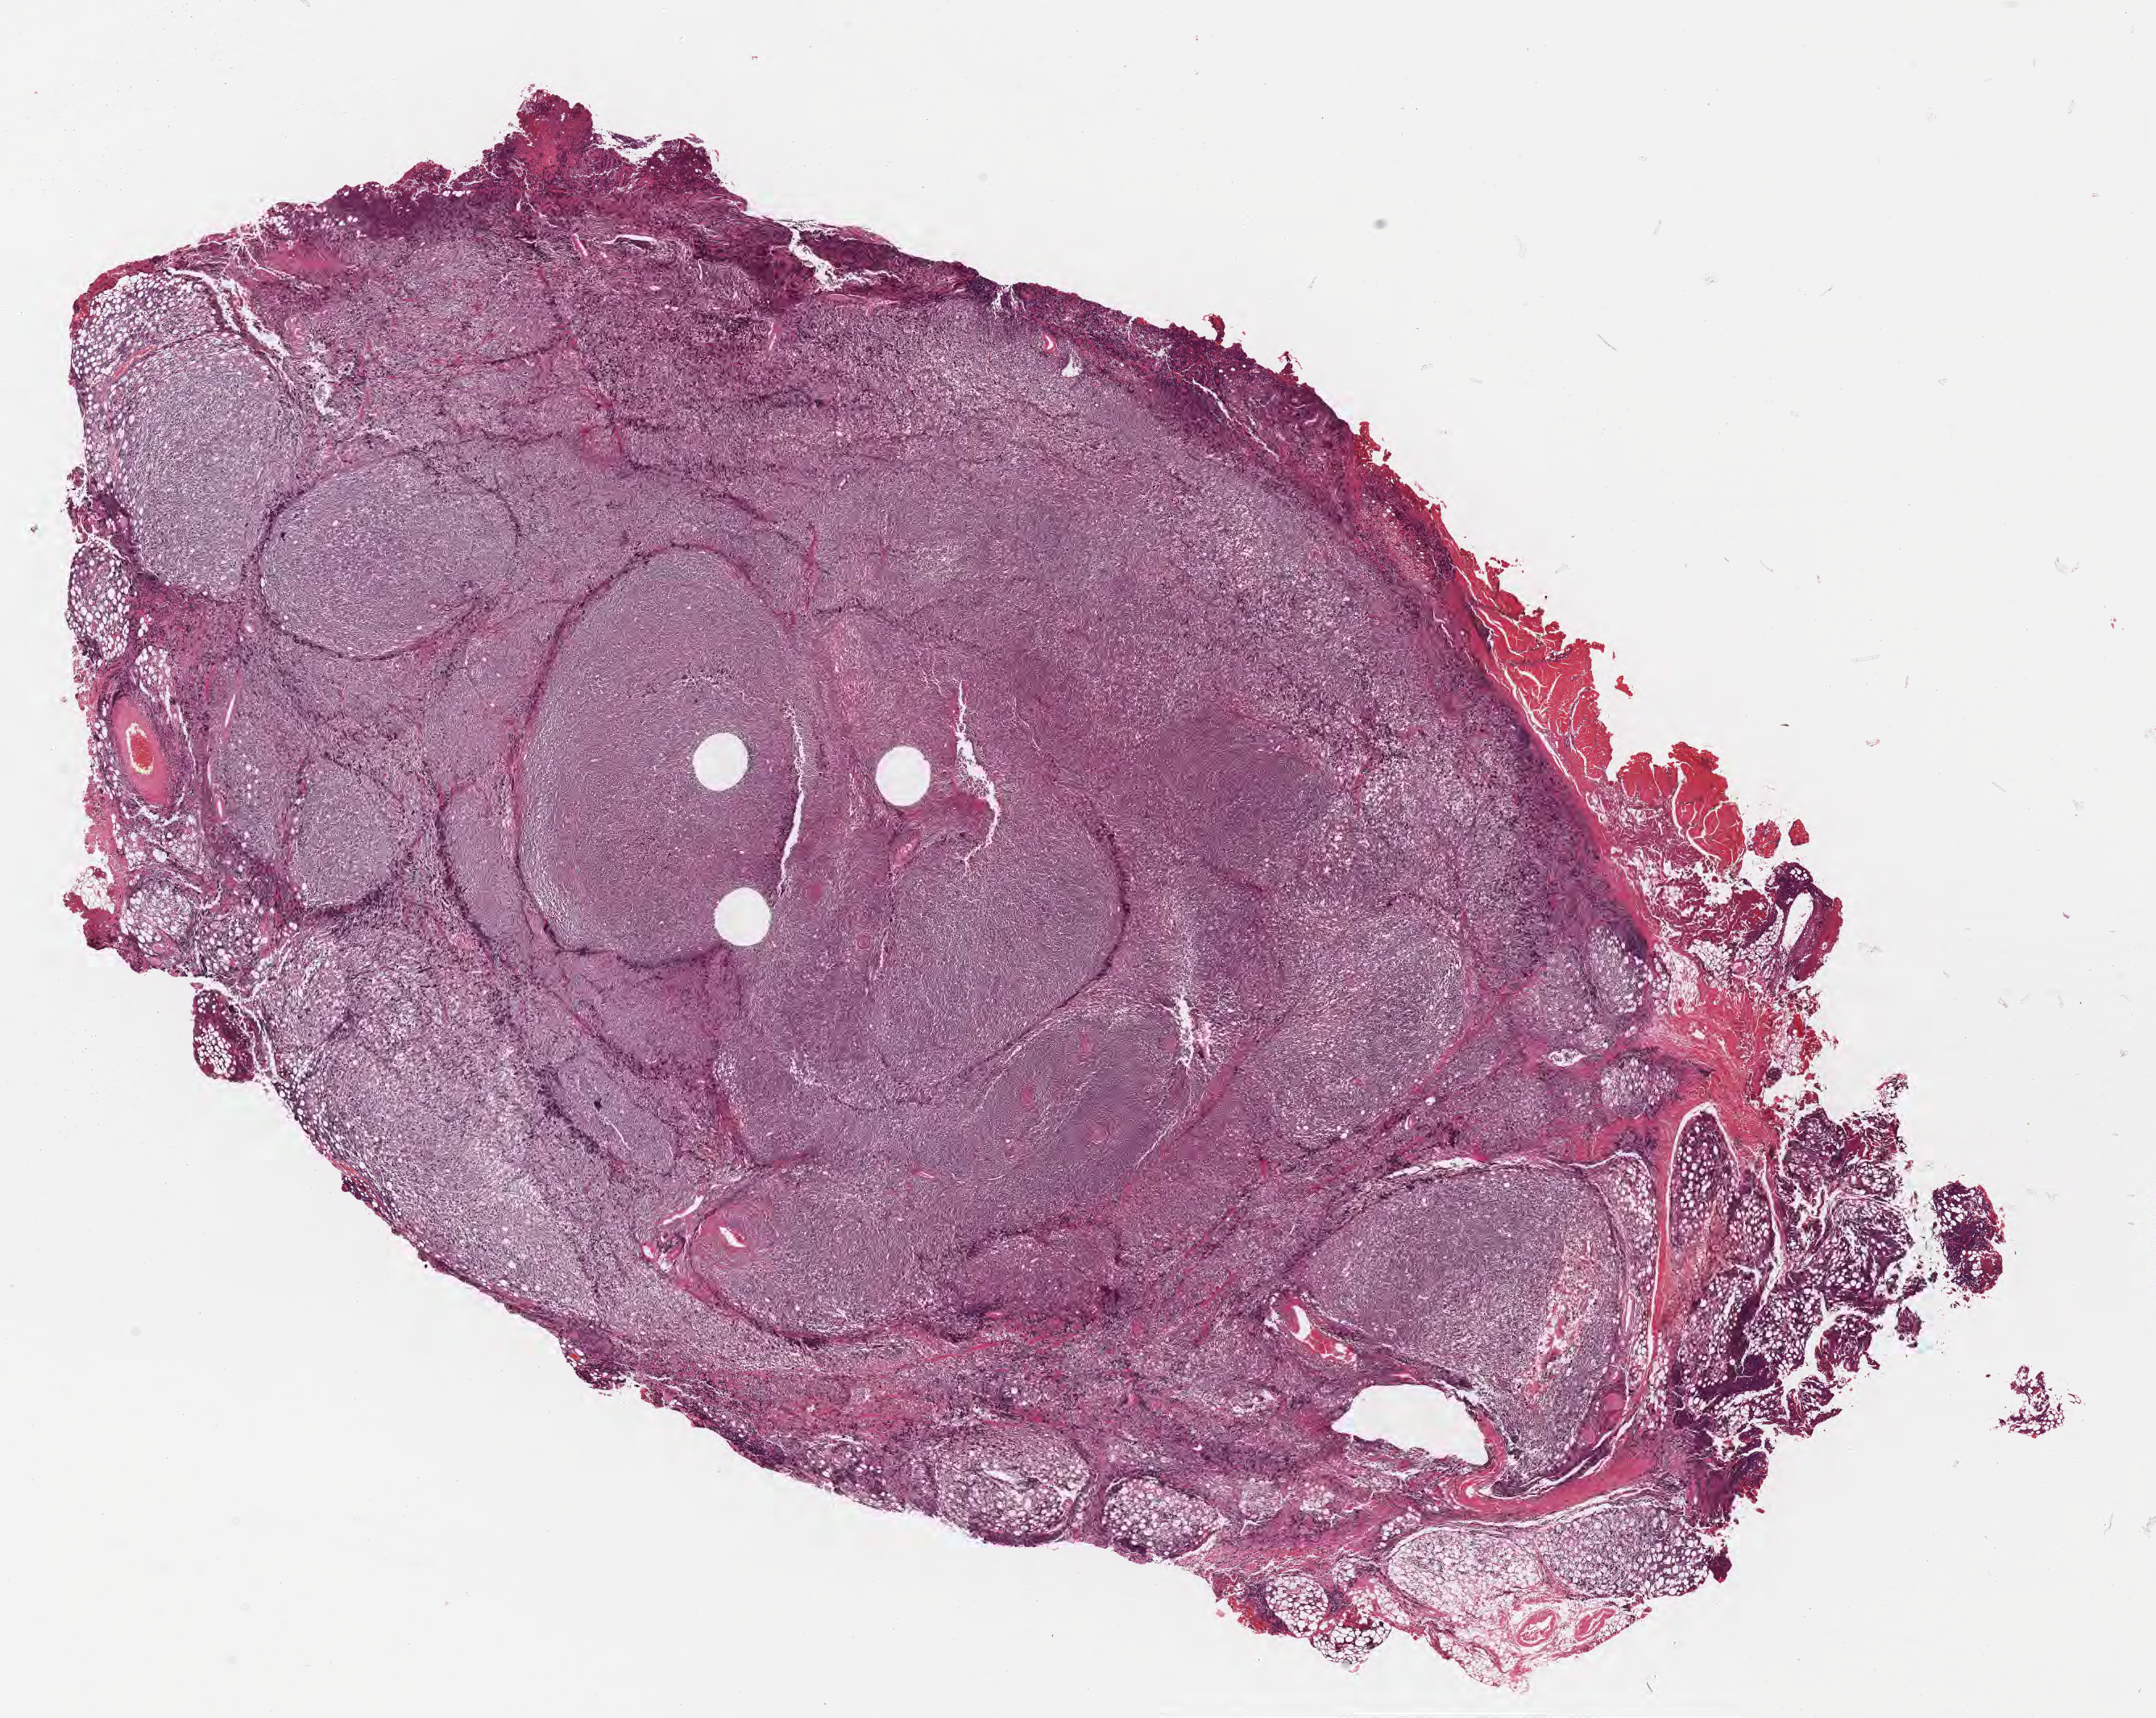
Digitized hematoxylin and eosin (H&E)-stained section — shown as a low-resolution overview of the whole scanned area (about 21.6 x 17.2 mm), FFPE section, primary tumor. Male, age 4 years at initial diagnosis. Slide review estimates, as recorded: tumor cells 85%, tumor nuclei 90%, stromal cells 10%, necrosis 0%, normal cells 5%. Inflammatory infiltration, as recorded: lymphocyte infiltration 75%, monocyte infiltration 15%, neutrophil infiltration 0%.
Ann Arbor stage (patient): Stage III. Diagnosis: Burkitt lymphoma, NOS.